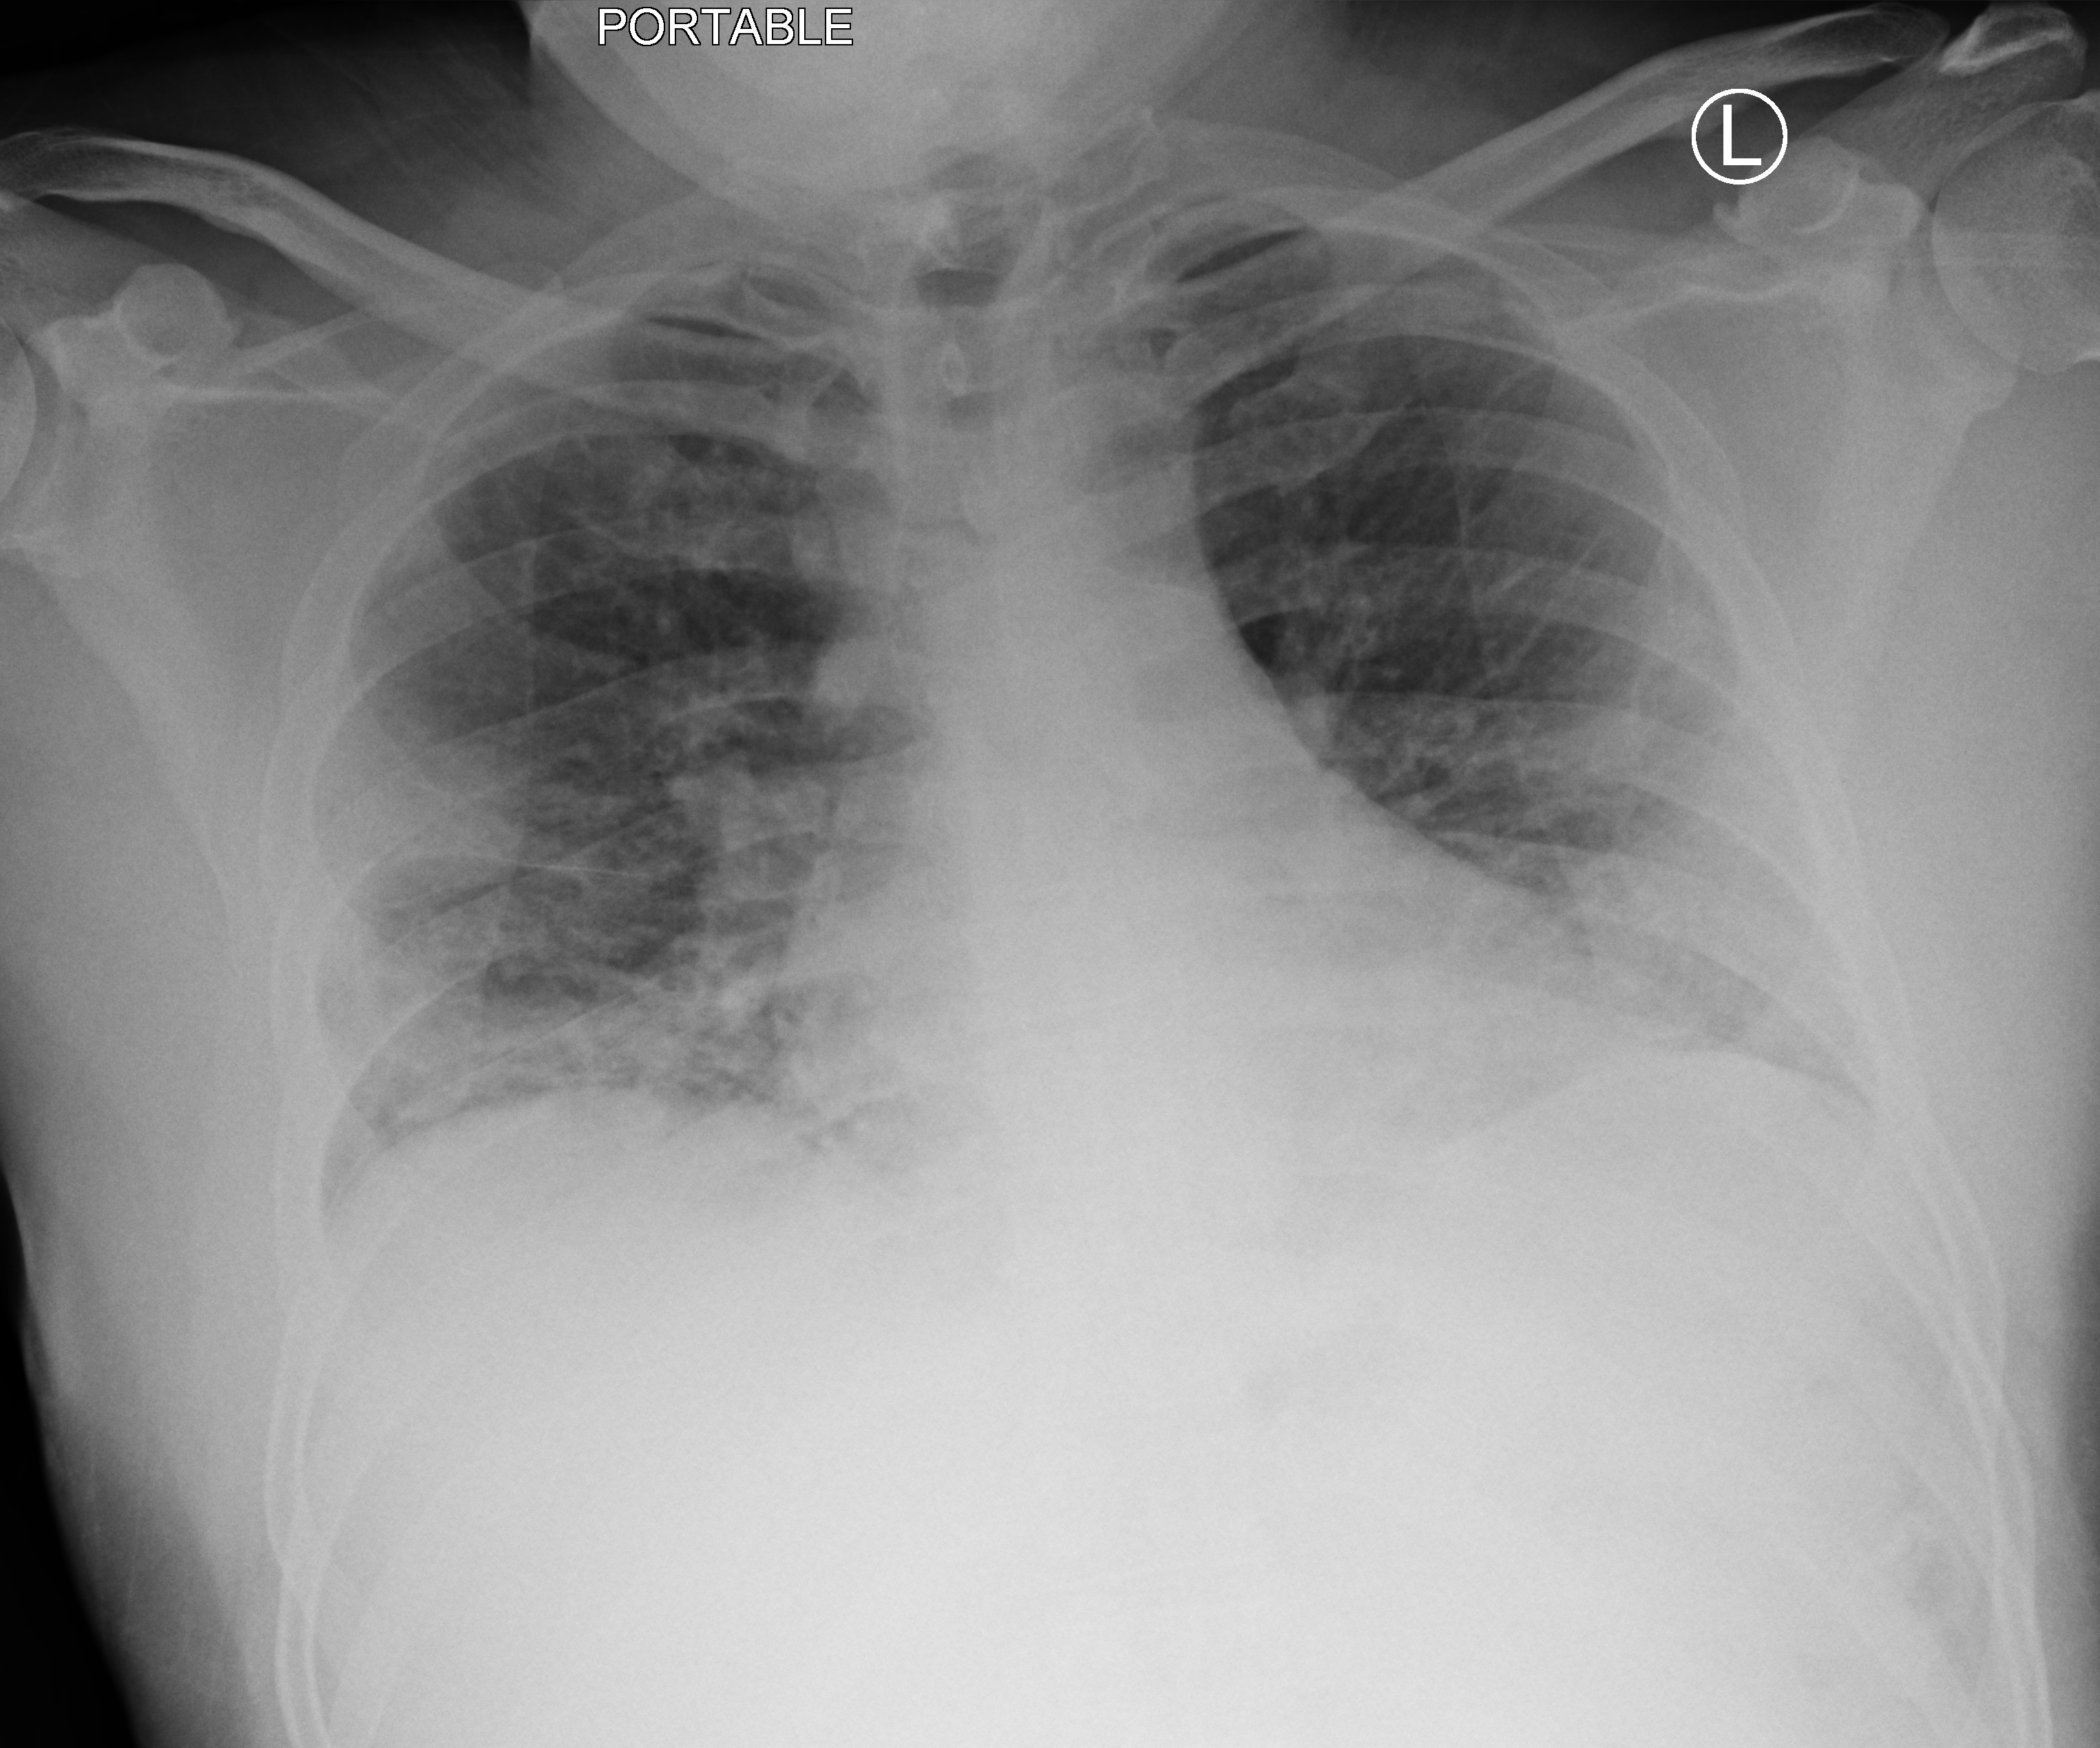
Portable chest radiograph, anteroposterior (AP) projection. Male patient hospitalised with COVID-19, age 18–59 years.
From the hospital-stay record, not from the radiograph (when in the stay this image was taken is not recorded): mechanically ventilated during this hospital stay: no; admitted to intensive care during this hospital stay: no.